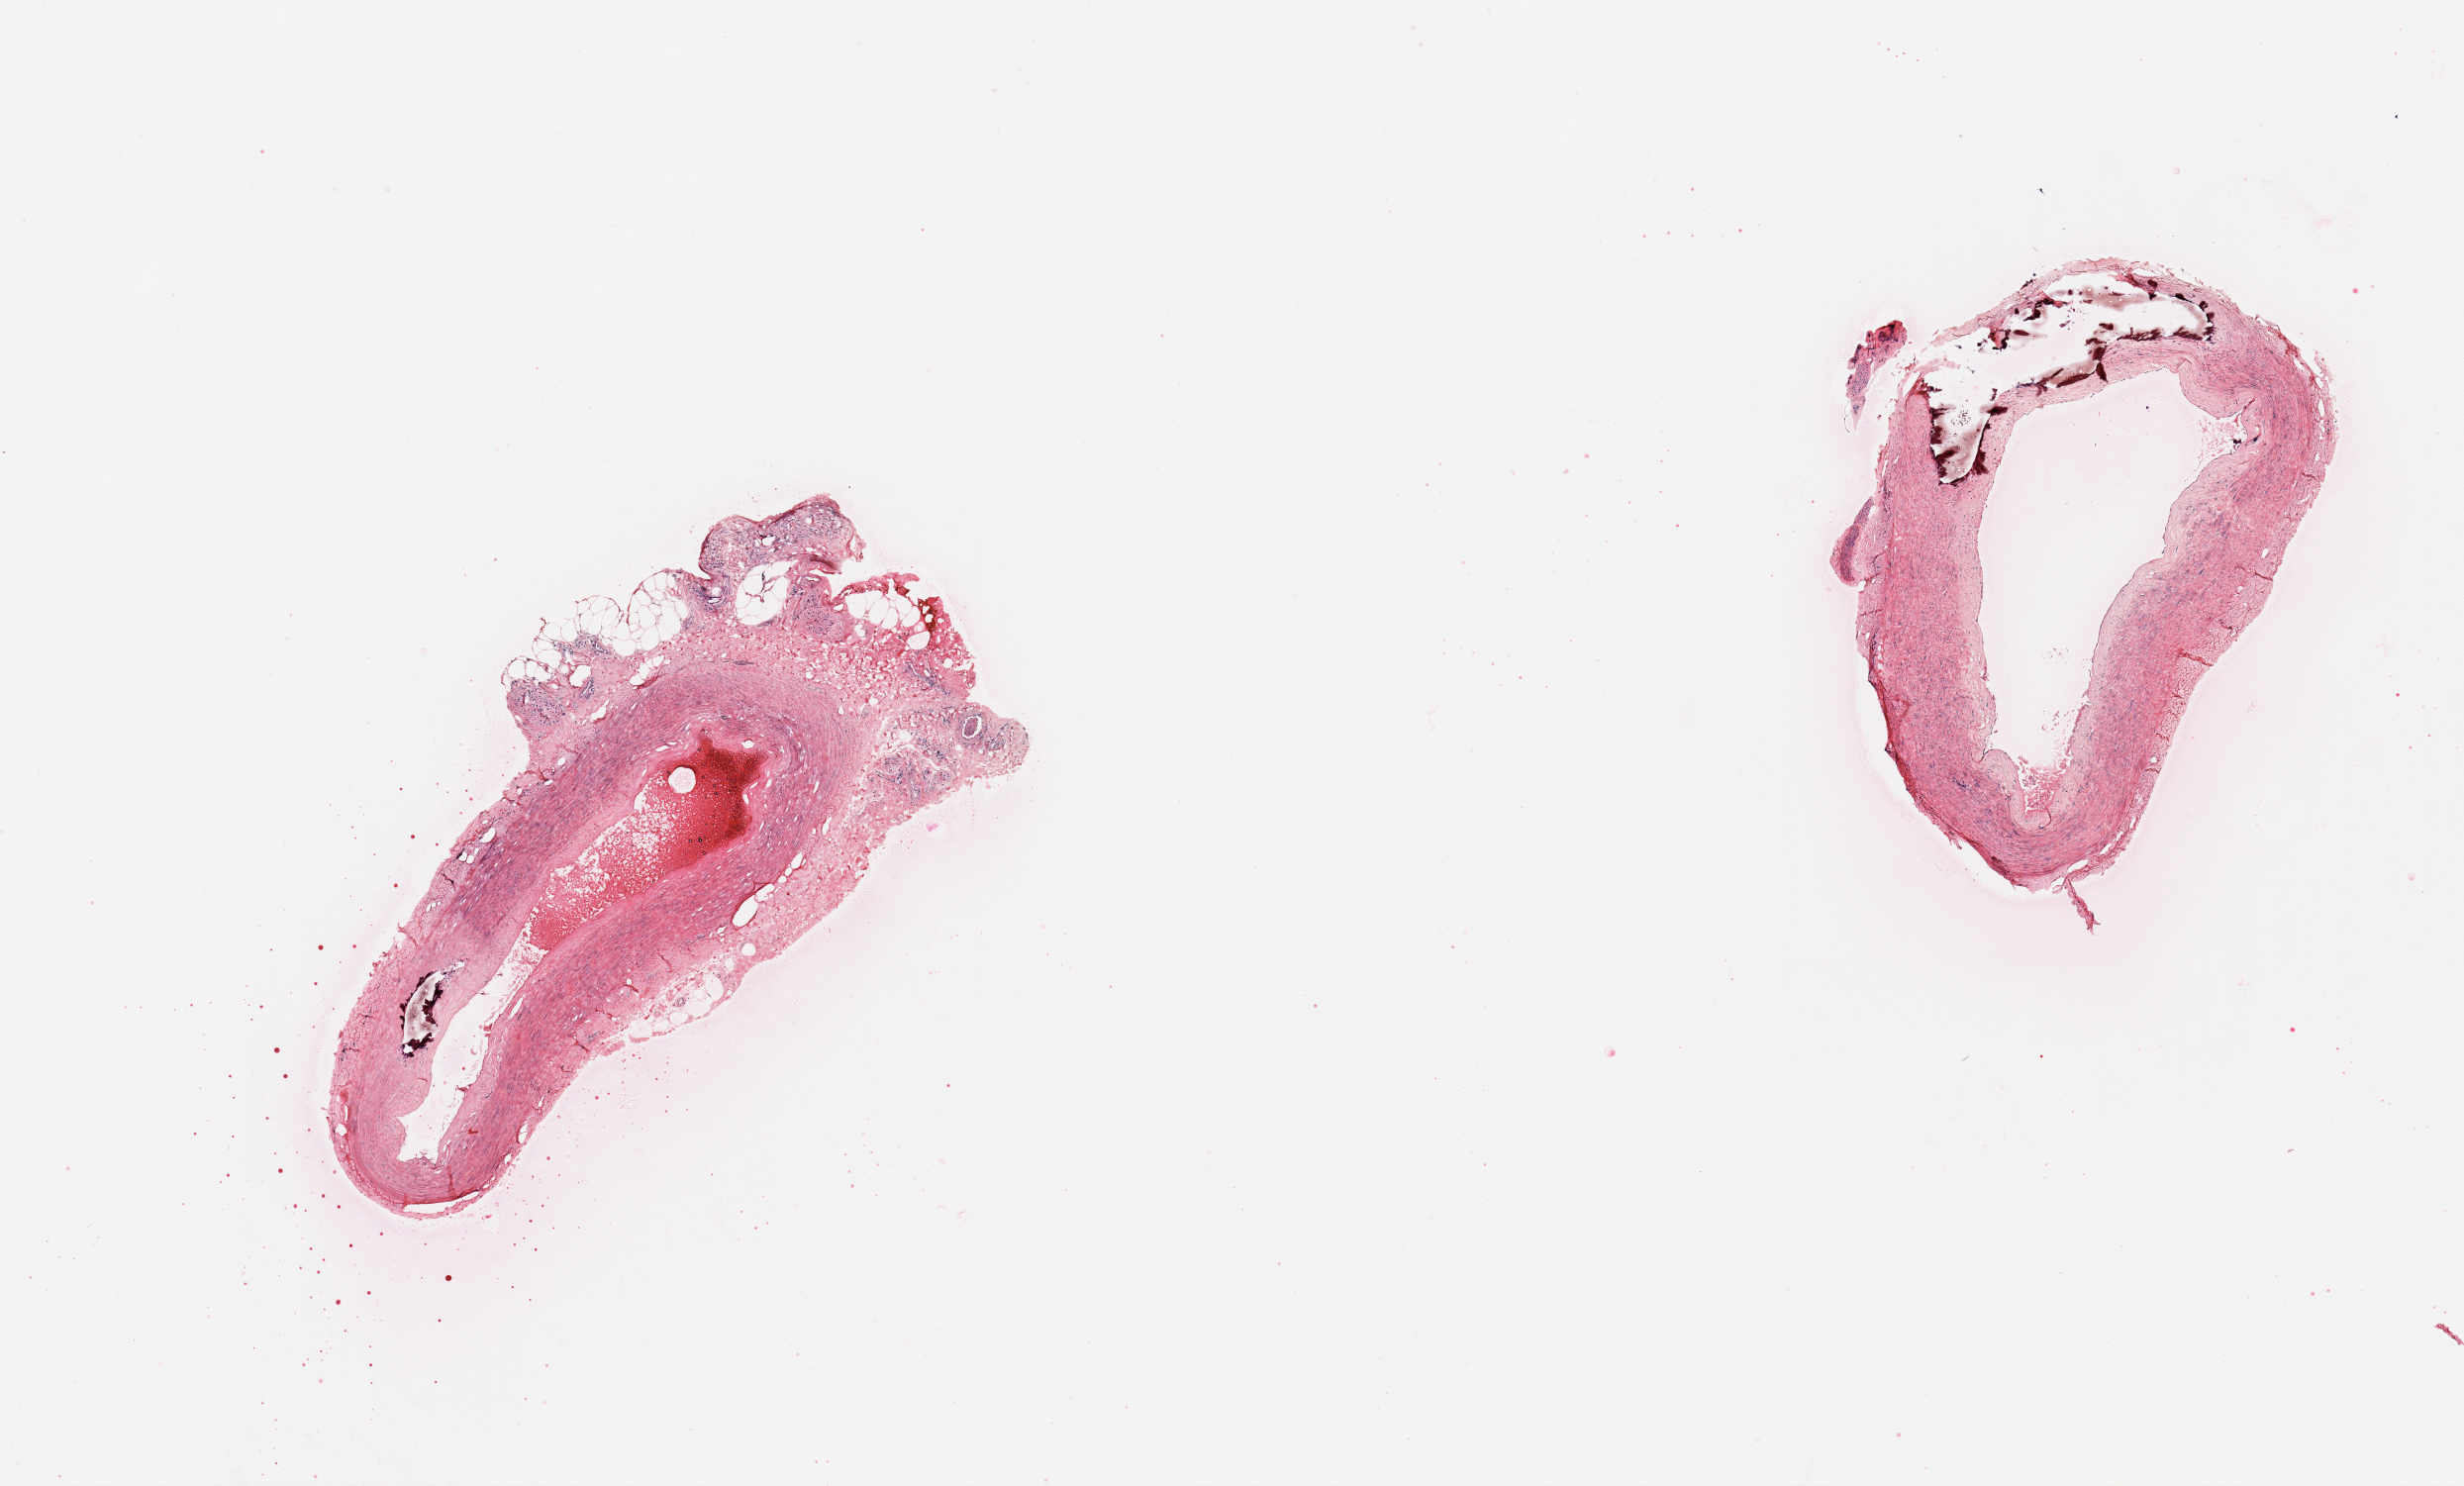
Whole-slide image, hematoxylin and eosin (H&E) stain — shown as a low-resolution overview of the whole scanned area (about 9.8 x 5.9 mm, from a 20x scan). PAXgene-fixed, paraffin-embedded tissue. Target tissue: tibial artery. Donor tissue sample. Donor sex: male.
Pathologist's review note for this sample: 2 pieces; fibrous plaque and medial calcification; ~0.5 mm attached adventitia.